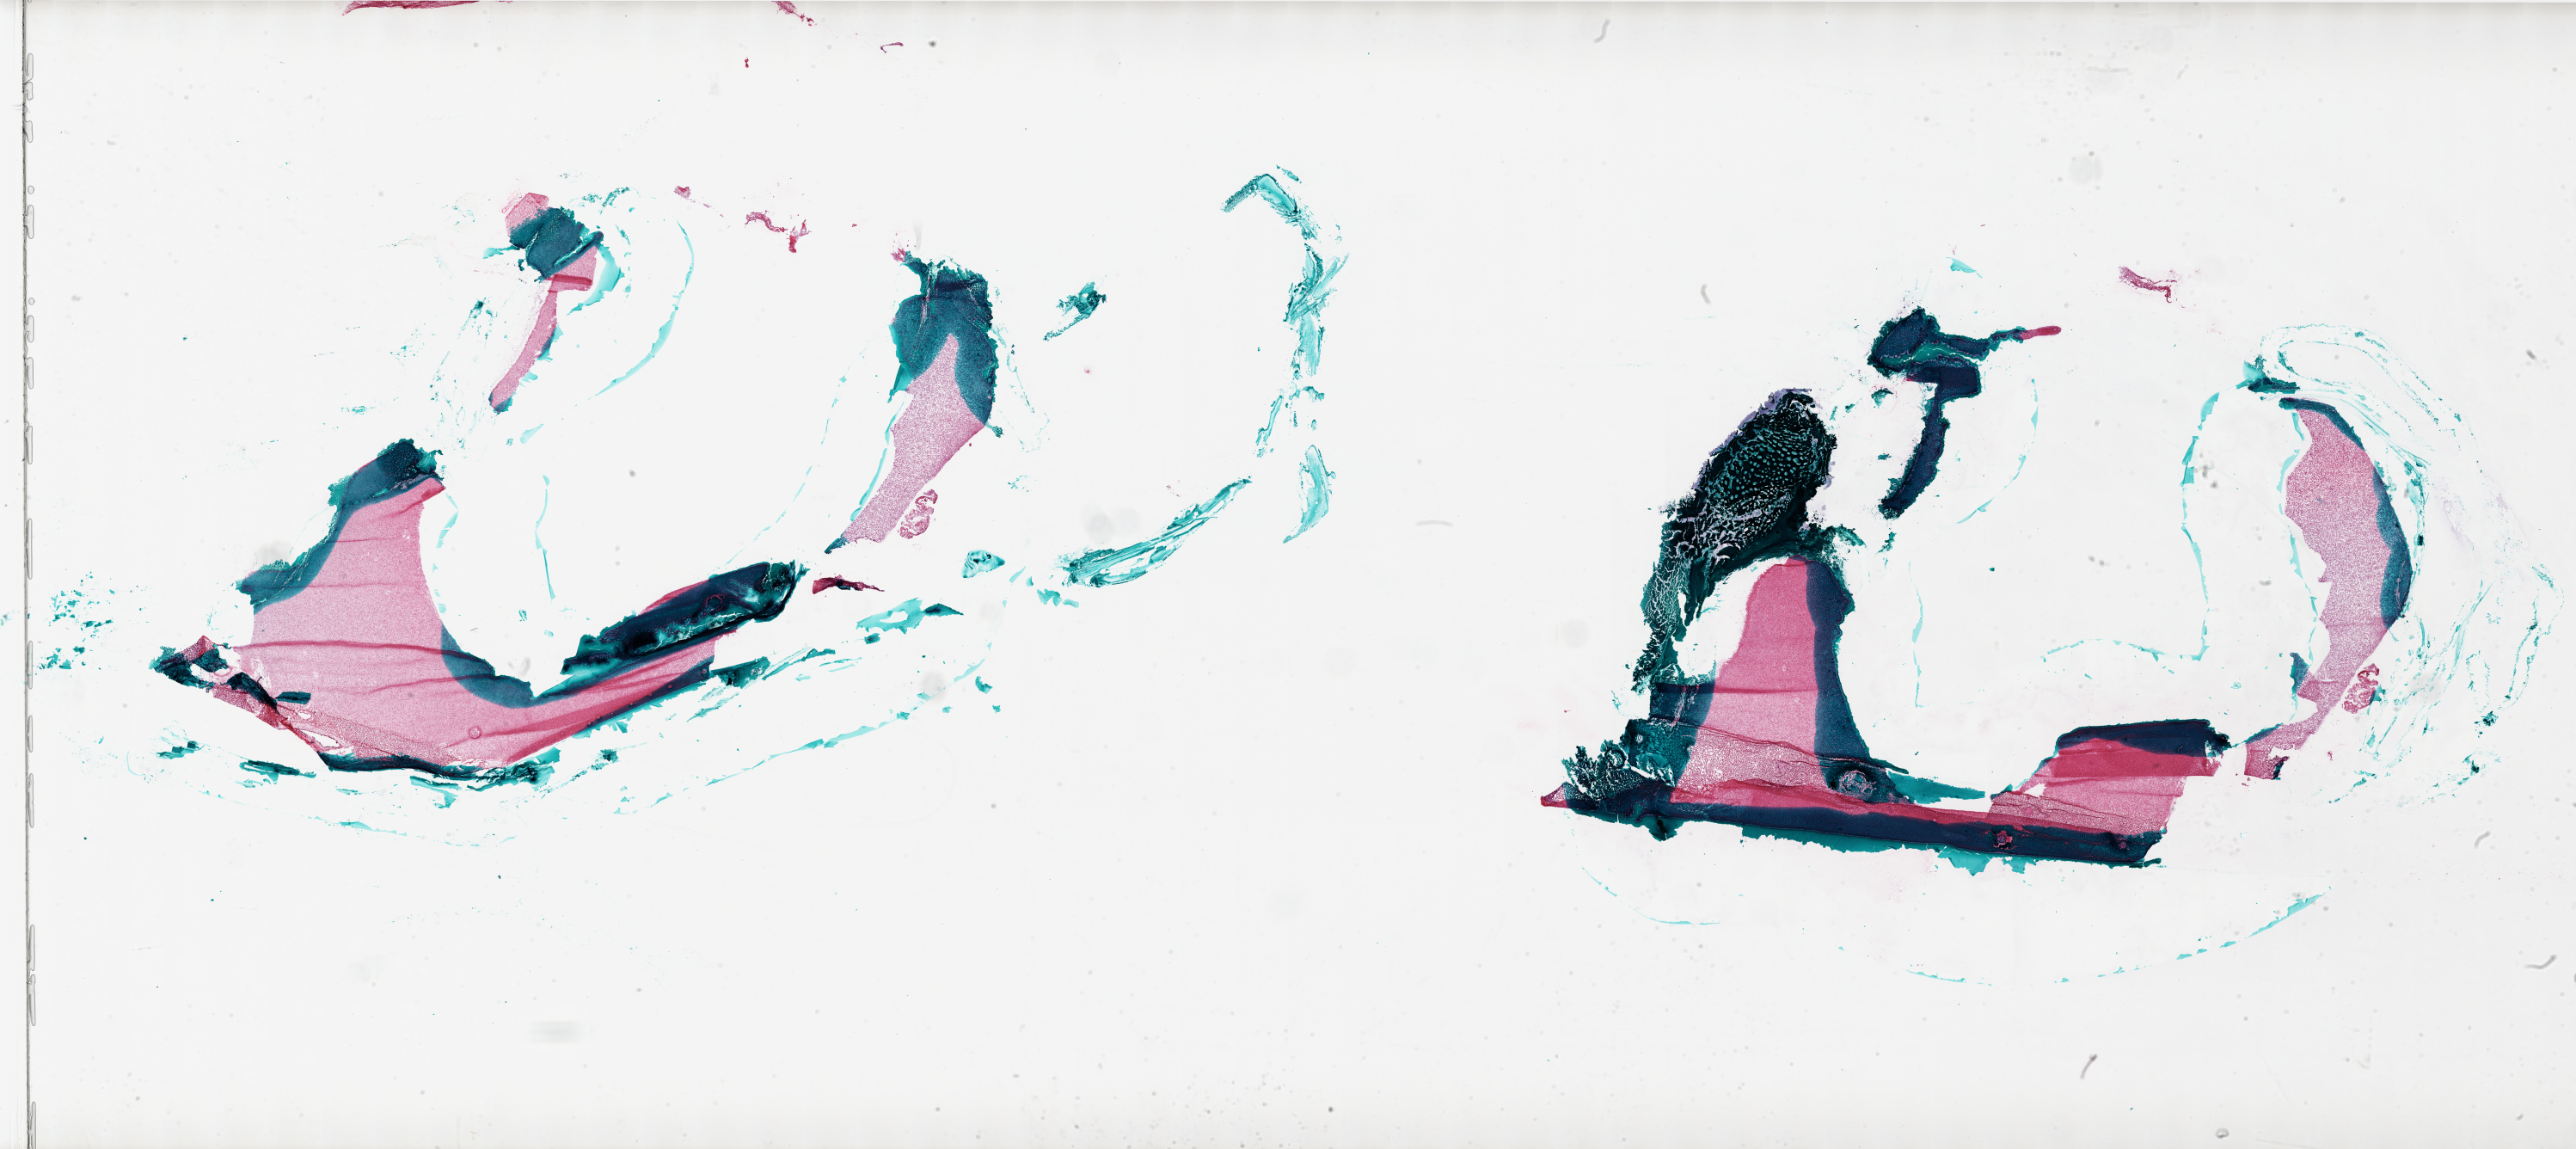
Digitized H&E-stained tissue section (whole slide) — a low-resolution overview of the entire scanned area, about 48.0 x 21.4 mm; frozen section; primary tumour sample from the brain. Patient: female, age at initial diagnosis 28 years. Composition of this section per pathologist review: tumour cells 100%, tumour nuclei 100%, normal cells 0%, stromal cells 0%, necrosis 0%.
* pathologic diagnosis: Glioblastoma